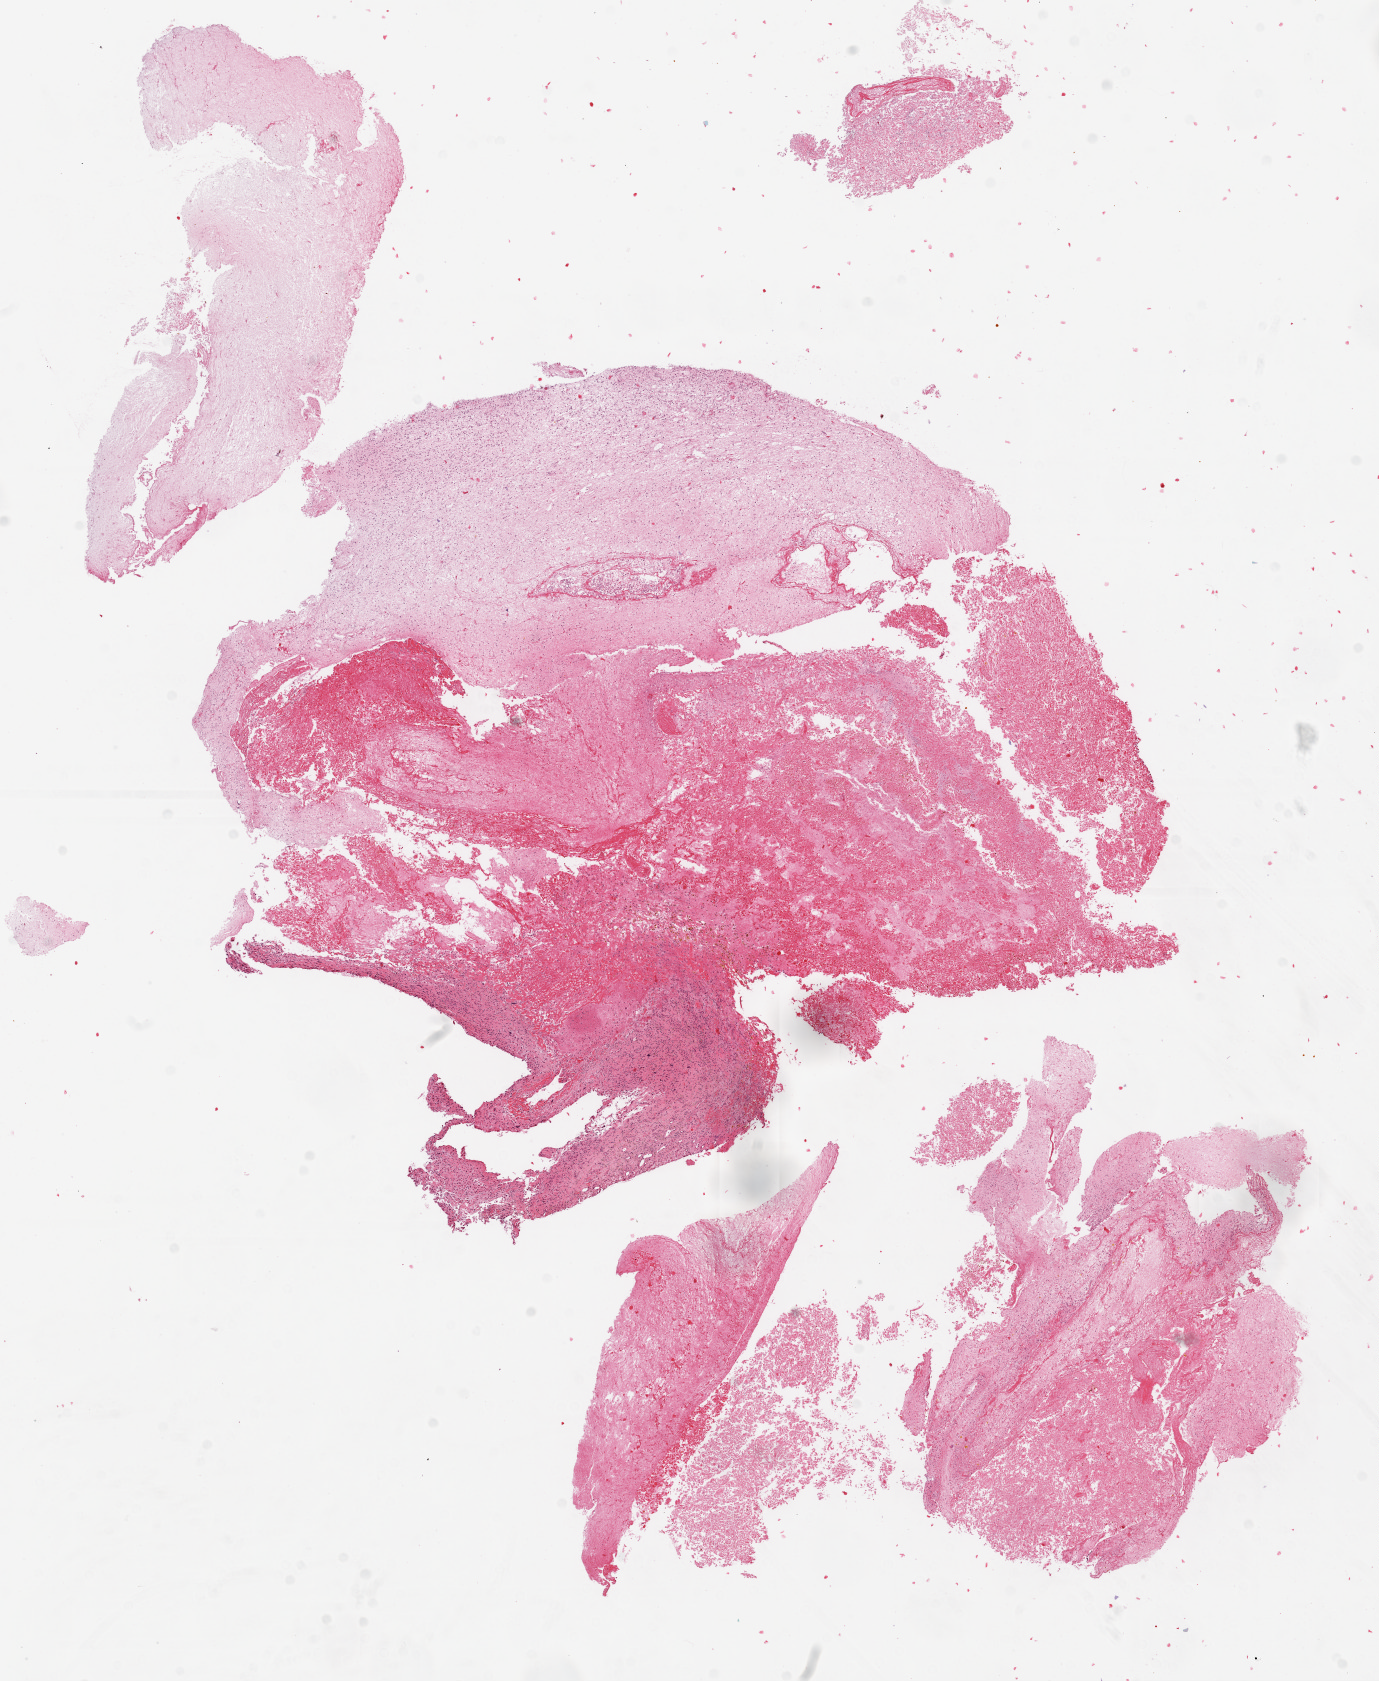
H&E whole-slide image, low-resolution overview of the scanned area, about 11.1 x 13.6 mm (slide scanned at 20x). Formalin-fixed paraffin-embedded (FFPE) diagnostic section. Brain, primary tumour sample. Female patient; age at initial diagnosis 69 years.
Histologic diagnosis: Glioblastoma.